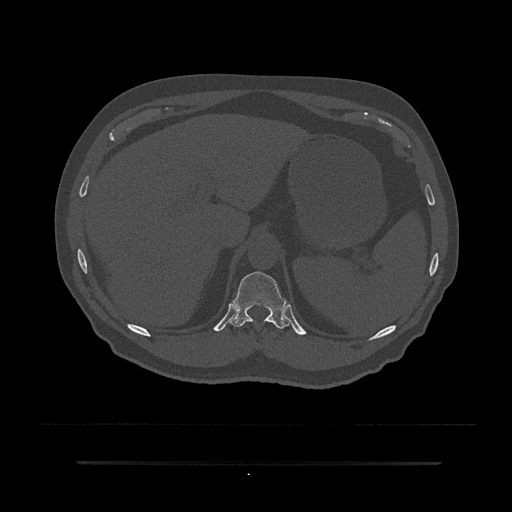
CT including the spine, one axial slice. Position 280 of 797 along the scan axis. Bone window (W 1800 / L 400 HU). 0.5 mm slice thickness. 512 × 512 image matrix, field of view 464 × 464 mm. Male patient, age 59 years. From the clinical record (not read from this slice): primary cancer: bile ducts; vertebrae with lytic lesions (as recorded): T10.
Structures marked on this image (semi-automatically segmented with operator editing):
- T11 vertebra: bounding box <230,271,294,329> (left, top, right, bottom; pixels)